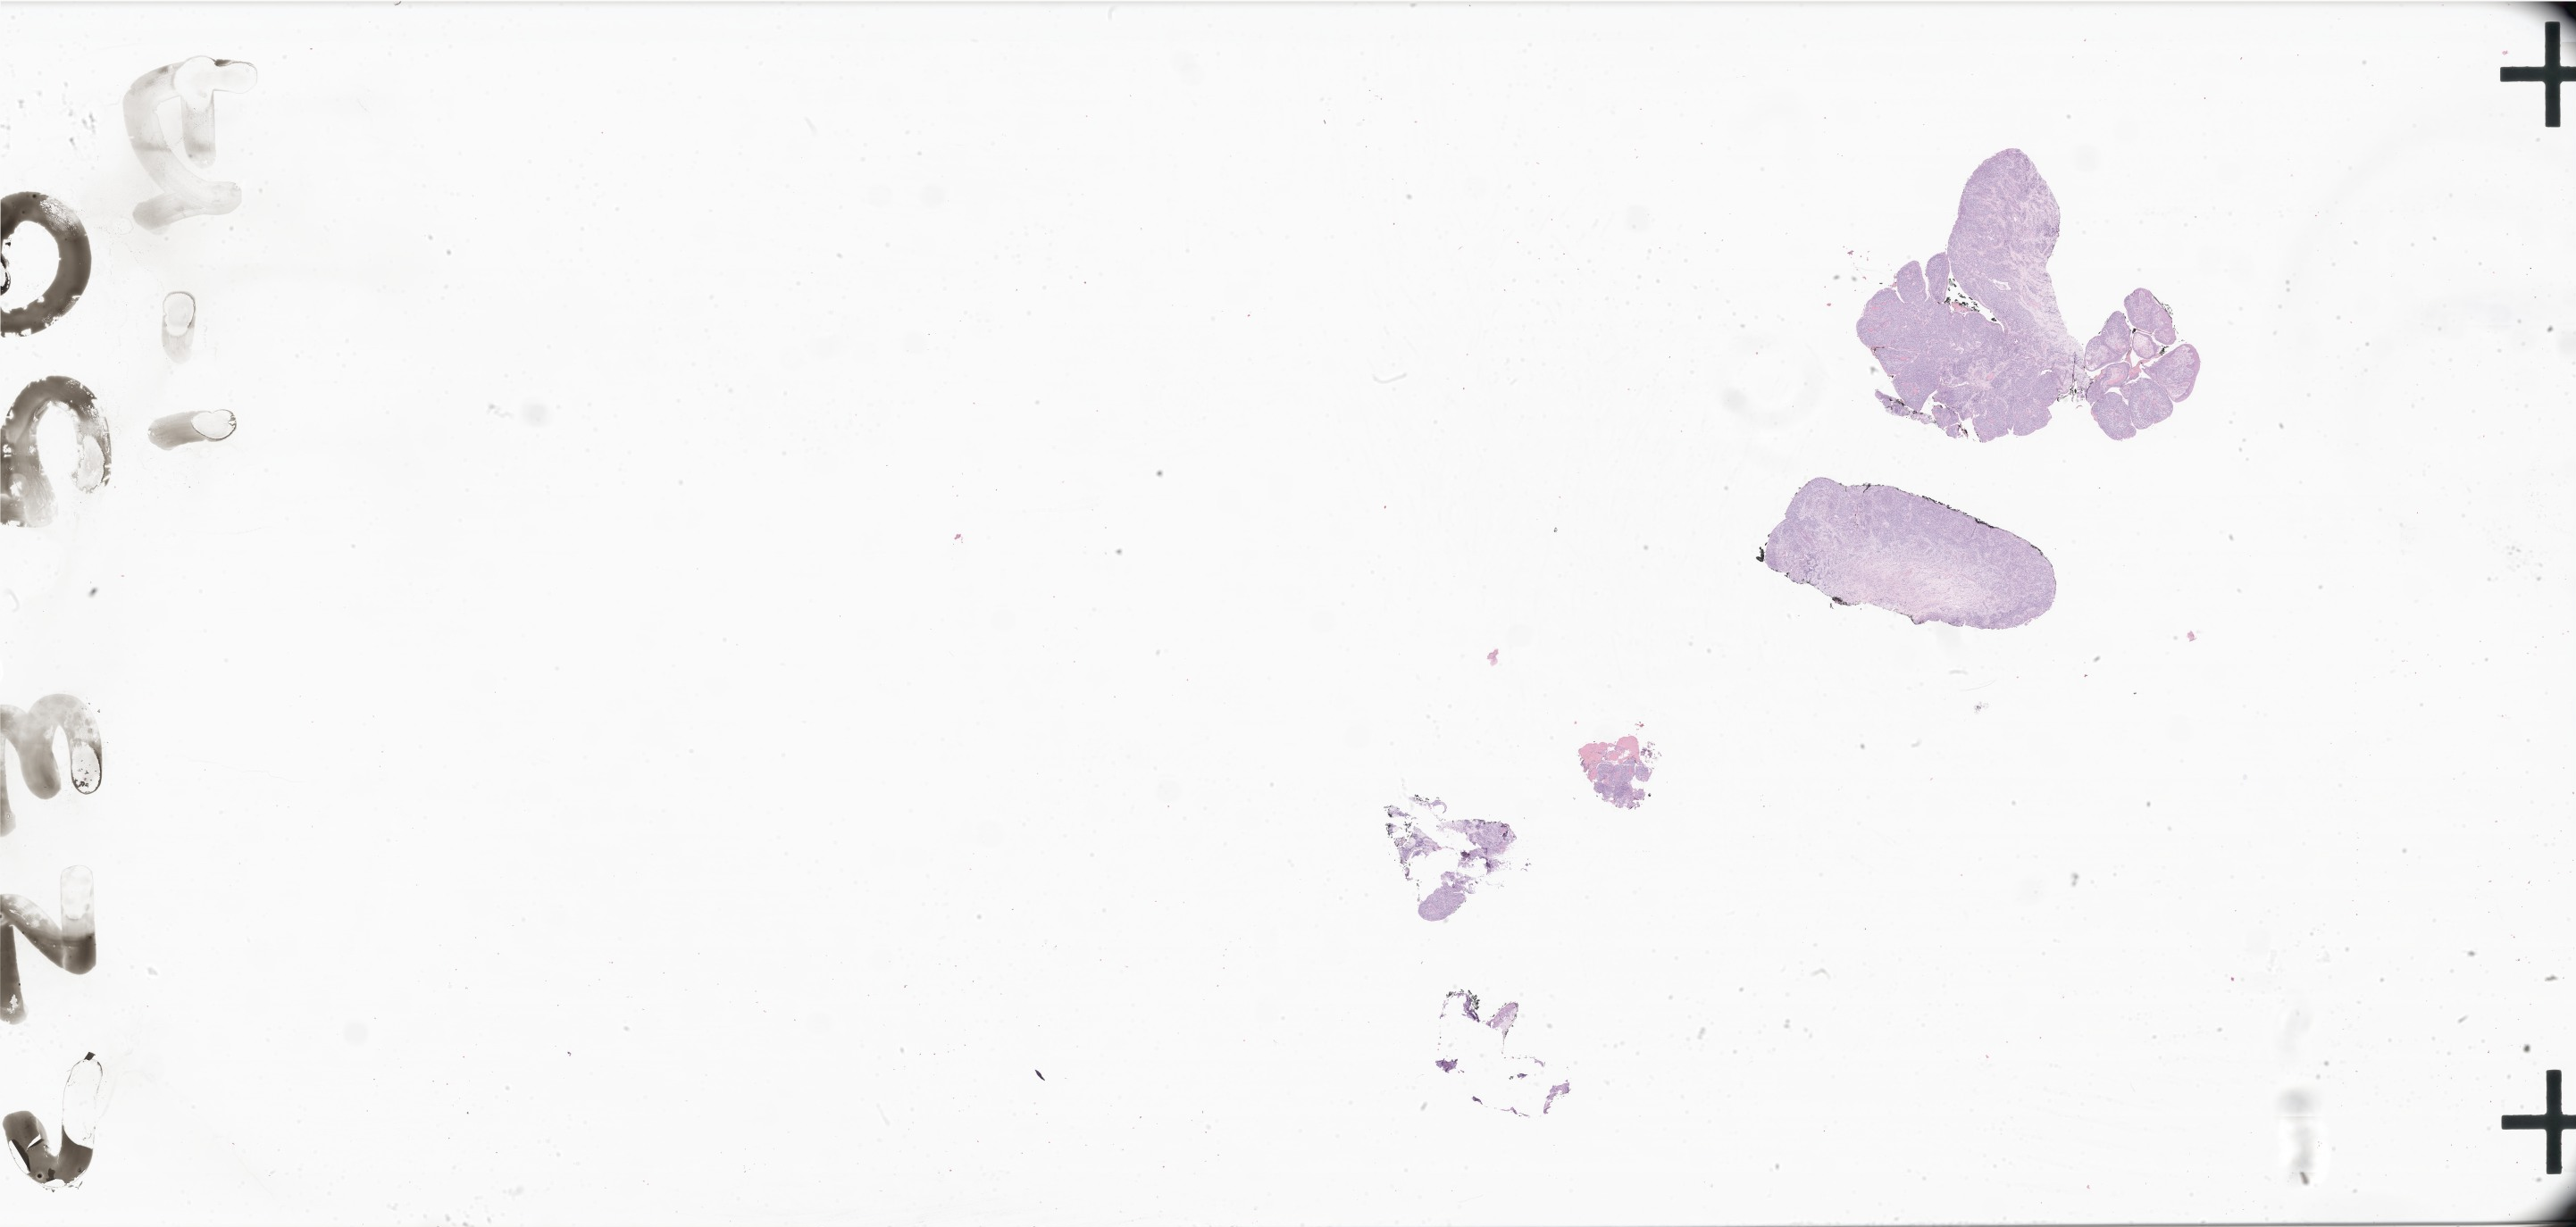
Whole-slide image, haematoxylin and eosin stain of tumor tissue from the eyelid — shown as a low-resolution overview of the whole scanned area (about 48.6 x 23.2 mm); formalin-fixed paraffin-embedded section. Female patient, age 100 months (8 years 4 months).
• diagnosis: Embryonal rhabdomyosarcoma, NOS